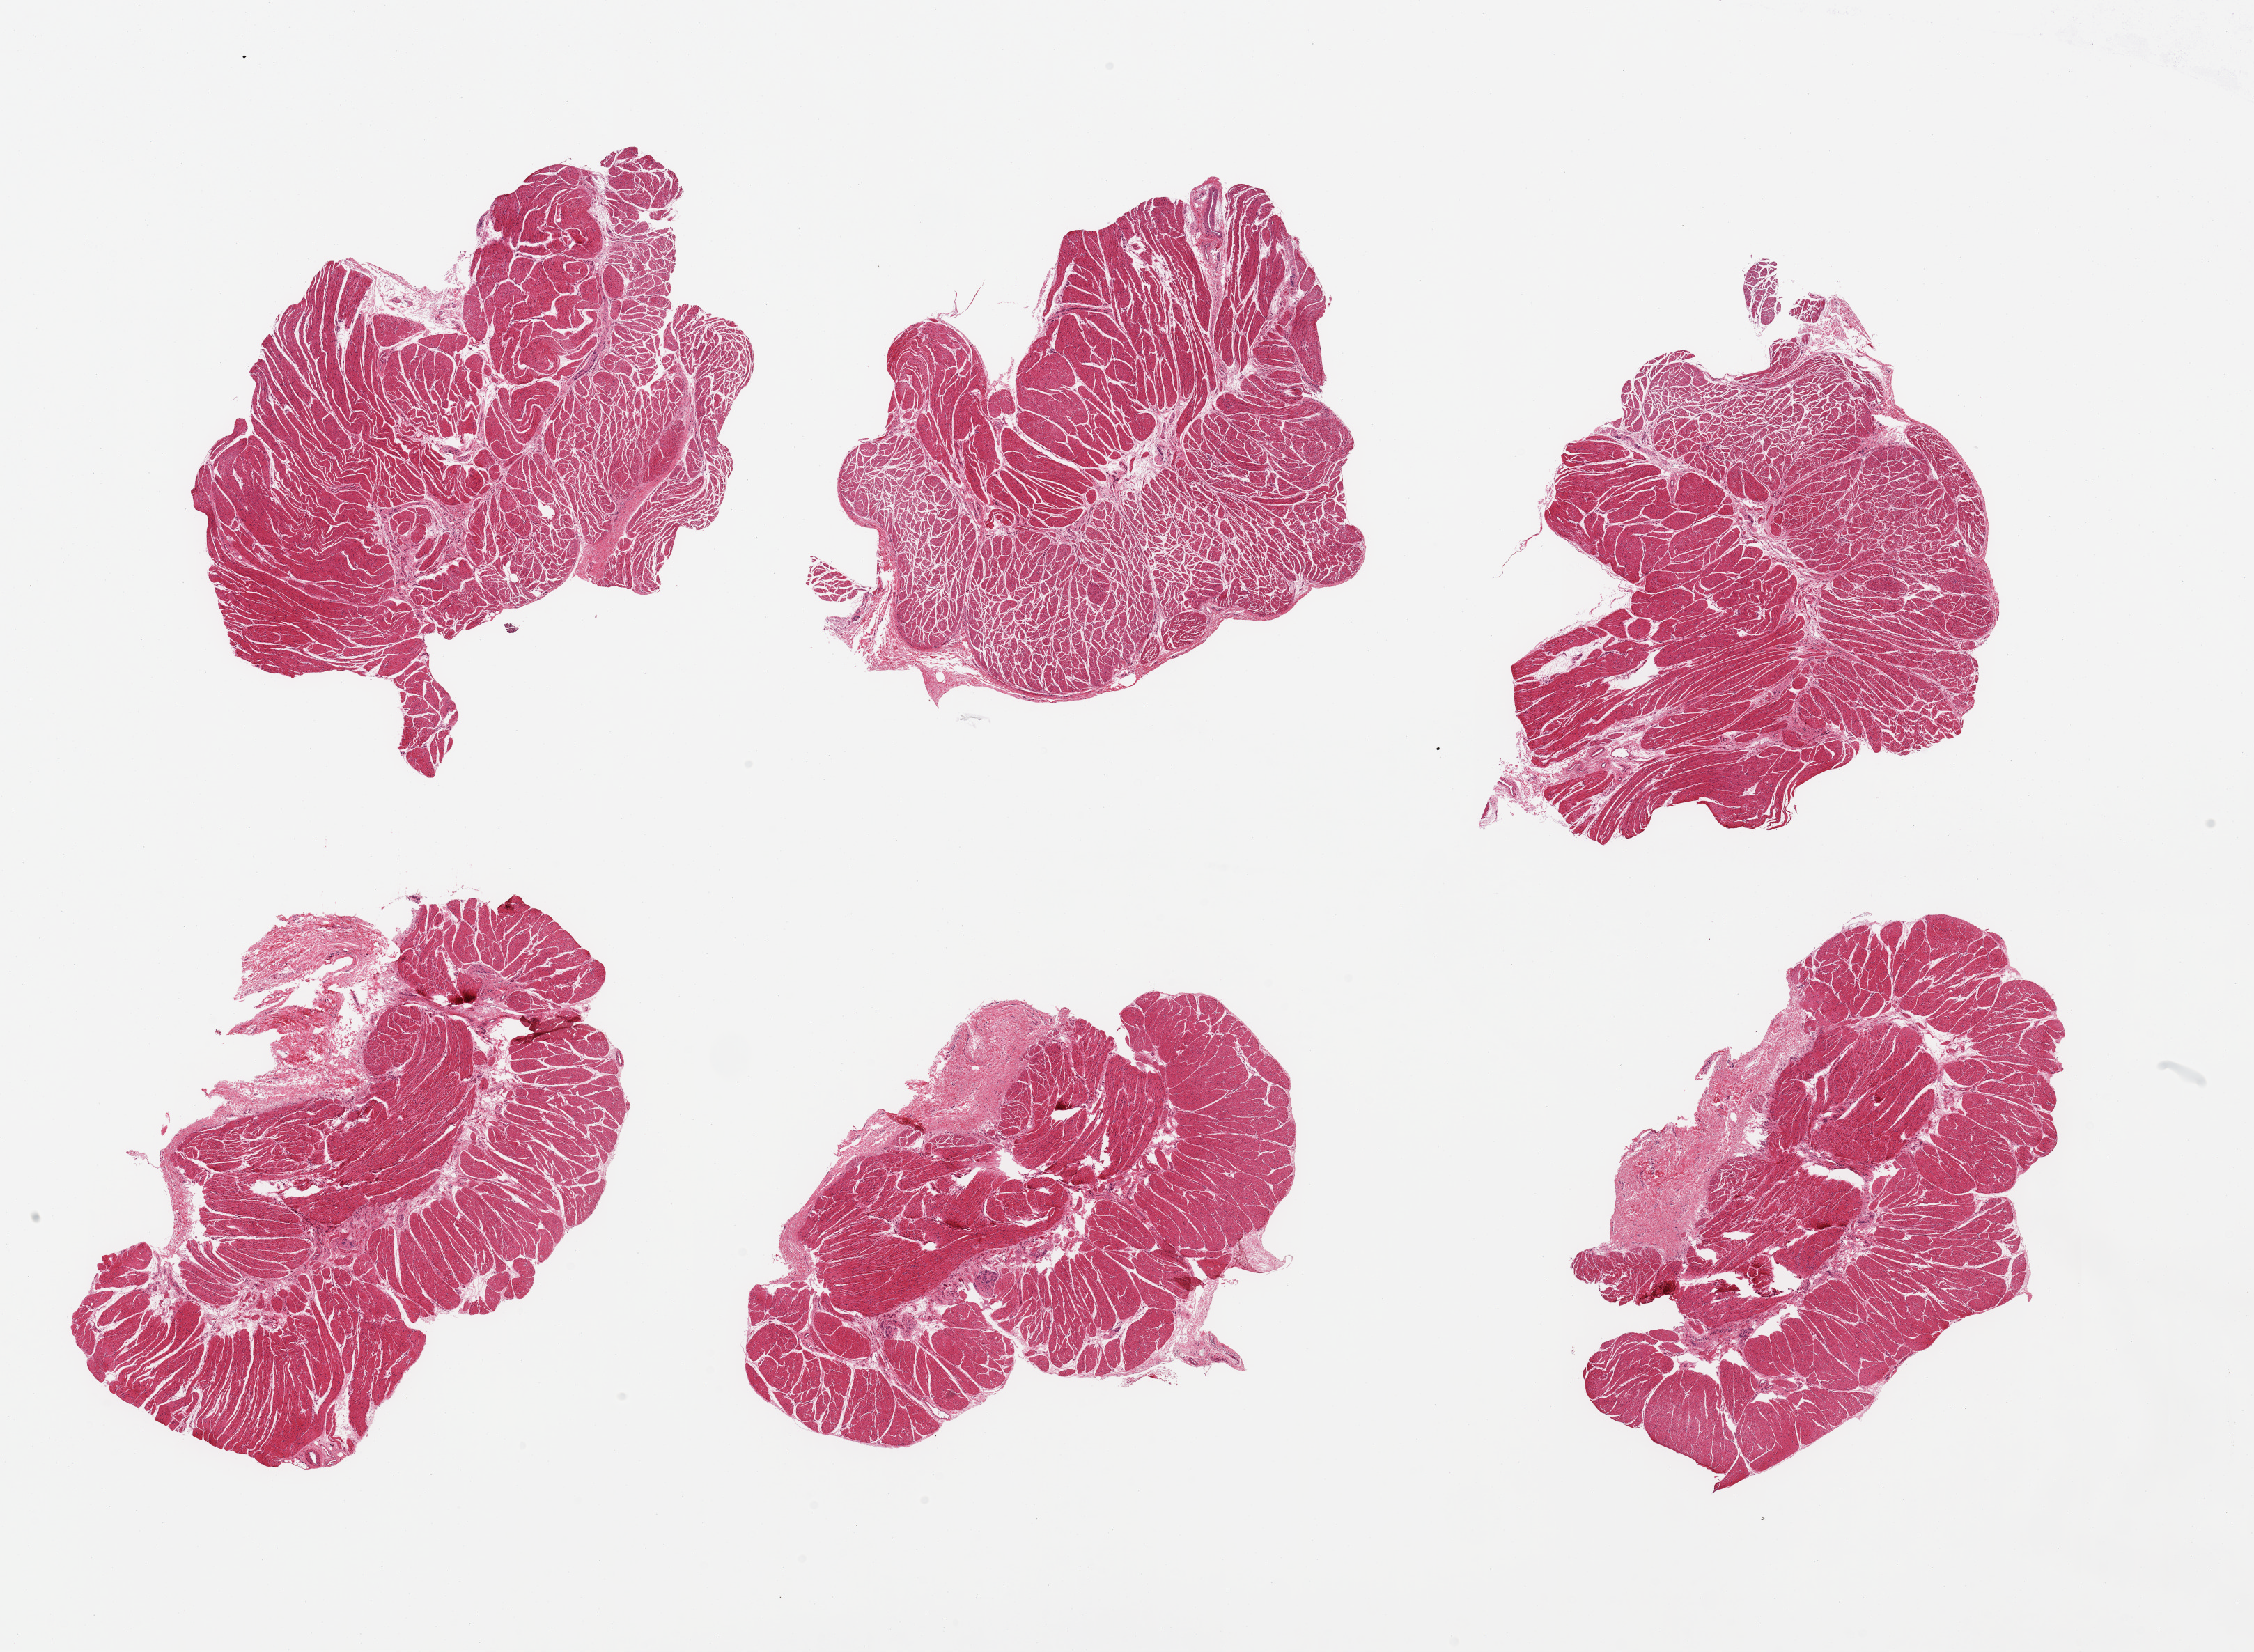
Digitized haematoxylin and eosin-stained section — whole scanned area (about 25.6 x 18.8 mm) shown as a low-resolution overview. PAXgene-fixed, paraffin-embedded tissue. Sampled site (target tissue): esophageal muscle. Donor tissue sample. Donor sex: male.
- review note (as recorded): 6 pieces; well dissected